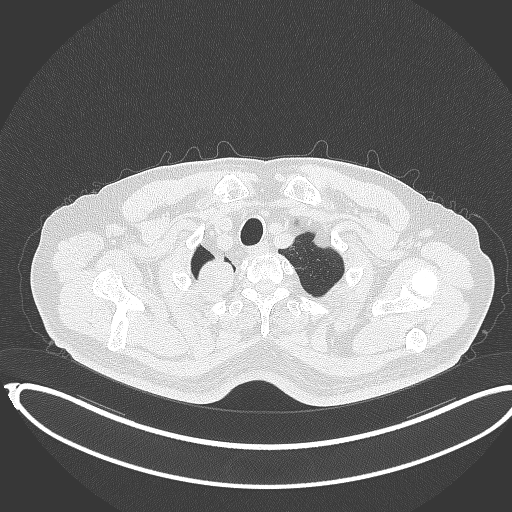
Chest CT, one axial slice. Position 340 of 403 along the scan axis. 120 kVp. Lung window (W 1500 / L -600 HU). 1 mm slice thickness. 512 × 512 image matrix. Male patient, age 68 years. From the clinical record (not read from this slice): clinical TNM (as recorded): T2a N0 M0.
Annotated regions visible in this slice (rectangle marked by the reading radiologist):
- lung tumour (recorded histology: adenocarcinoma): bounding box (x1, y1, x2, y2) in pixels: (196, 257, 237, 300)